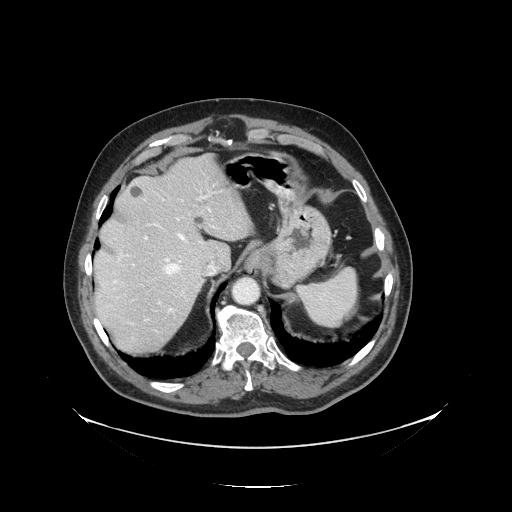
Contrast-enhanced abdominal CT, one axial slice; reconstruction kernel STANDARD; 120 kVp; soft-tissue window (W 400 / L 40 HU); 2.5 mm slice thickness; 512 × 512 image matrix. Male patient, age 77 years. Case-level facts recorded for this patient, not image findings: diagnosis: colorectal cancer liver metastases, imaged before liver resection; multiple liver metastases: no; largest metastasis: 1.5 cm; chemotherapy before resection: no.
Outlined on this slice (outlined manually by an expert reader):
- hepatic veins: box from (x=155, y=207) to (x=213, y=312) px
- liver: (x=95, y=158)–(x=252, y=355)
- planned liver remnant (the part of the liver to remain after resection): (x=94, y=158)–(x=252, y=290)
- portal vein (with intrahepatic branches): (x=132, y=188)–(x=234, y=321)
- liver metastasis: (x=194, y=216)–(x=205, y=225)
- liver metastasis: (x=130, y=186)–(x=142, y=198)